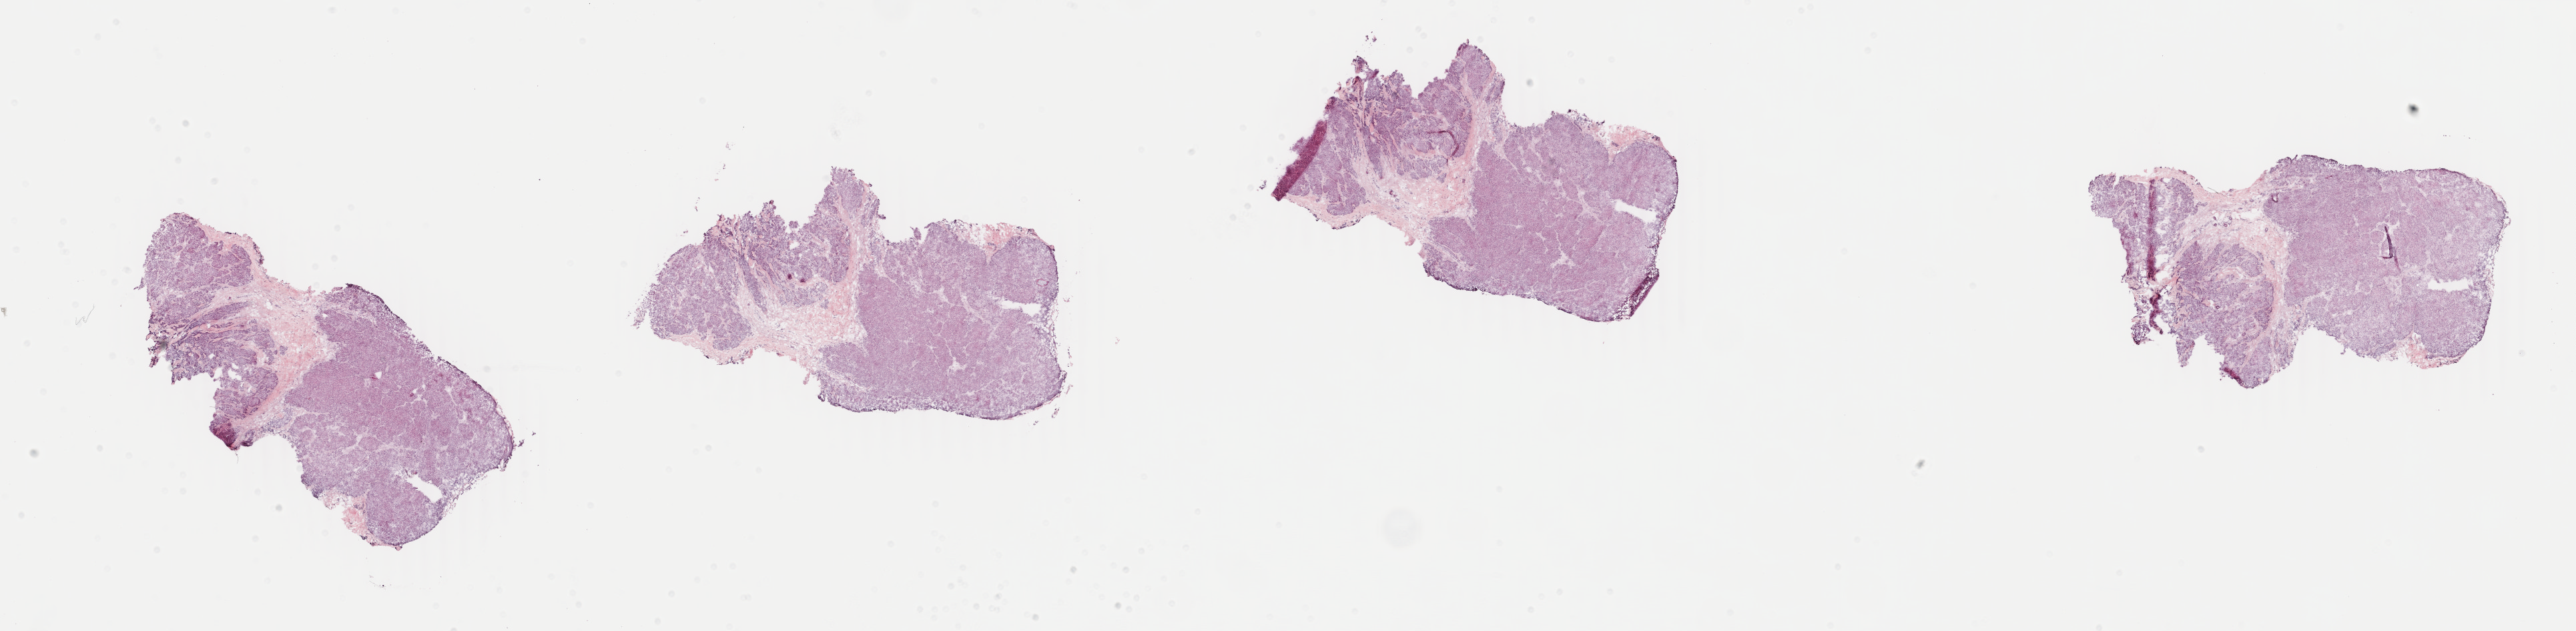
H&E whole-slide image — whole scanned area (about 30.7 x 7.5 mm, acquisition: 40x scan) shown as a low-resolution overview; frozen section from the top of the tissue portion; metastatic tumour sample. Patient: female, age at initial diagnosis 67 years.
This section: metastatic tumour tissue. Patient diagnosis: Malignant melanoma, NOS.